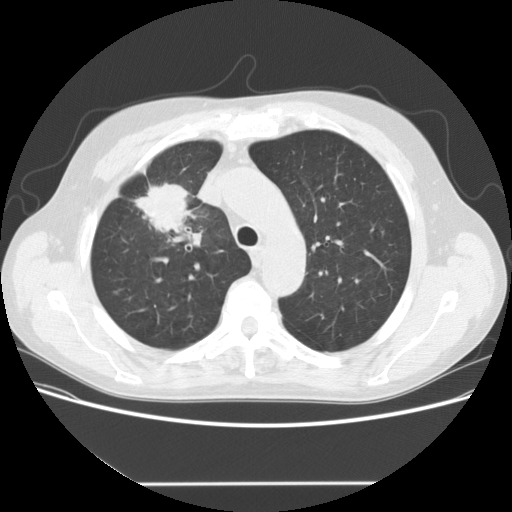
Low-dose screening chest CT, one axial slice. Slice 115 of 153 in the series (ordered by position). 120 kVp. Lung window (W 1500 / L -600 HU). 2.5 mm slice thickness. 512 × 512 image matrix.
Structures marked on this image (manually delineated by an expert):
- lesion 1 (tumor, upper lobe of right lung): box from (x=134, y=183) to (x=192, y=234) px